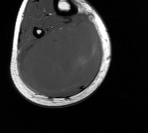
MRI of an extremity soft-tissue mass, one axial slice; position 51 of 76 along the scan axis; MR volume resampled by the dataset authors to the PET/CT grid (not the native acquisition matrix); 3.27 mm slice thickness; 148 × 133 image matrix, field of view 145 × 130 mm. Male patient. Case-level facts recorded for this patient, not image findings: histological type: liposarcoma - round cell; grade: high; site of the primary tumour: right calf.
Structures marked on this image (expert contour drawn on MRI and transferred to this co-registered scan by the dataset authors):
- gross tumour volume (mass): bounding box <22,23,100,95> (left, top, right, bottom; pixels)